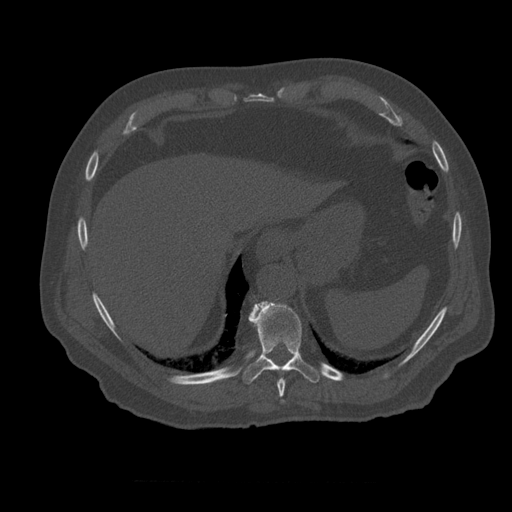
CT including the spine, one axial slice. Position 304 of 399 along the scan axis. Bone window (W 1800 / L 400 HU). 1.25 mm slice thickness. 512 × 512 image matrix, field of view 407 × 407 mm. Patient age 73 years. Case-level facts recorded for this patient, not image findings: primary cancer: prostate; vertebrae with lytic lesions (as recorded): L2.
Outlined on this slice (semi-automatically segmented with operator editing):
- T10 vertebra: bounding box <242,301,323,384> (left, top, right, bottom; pixels)
- T9 vertebra: <278,370,286,404>